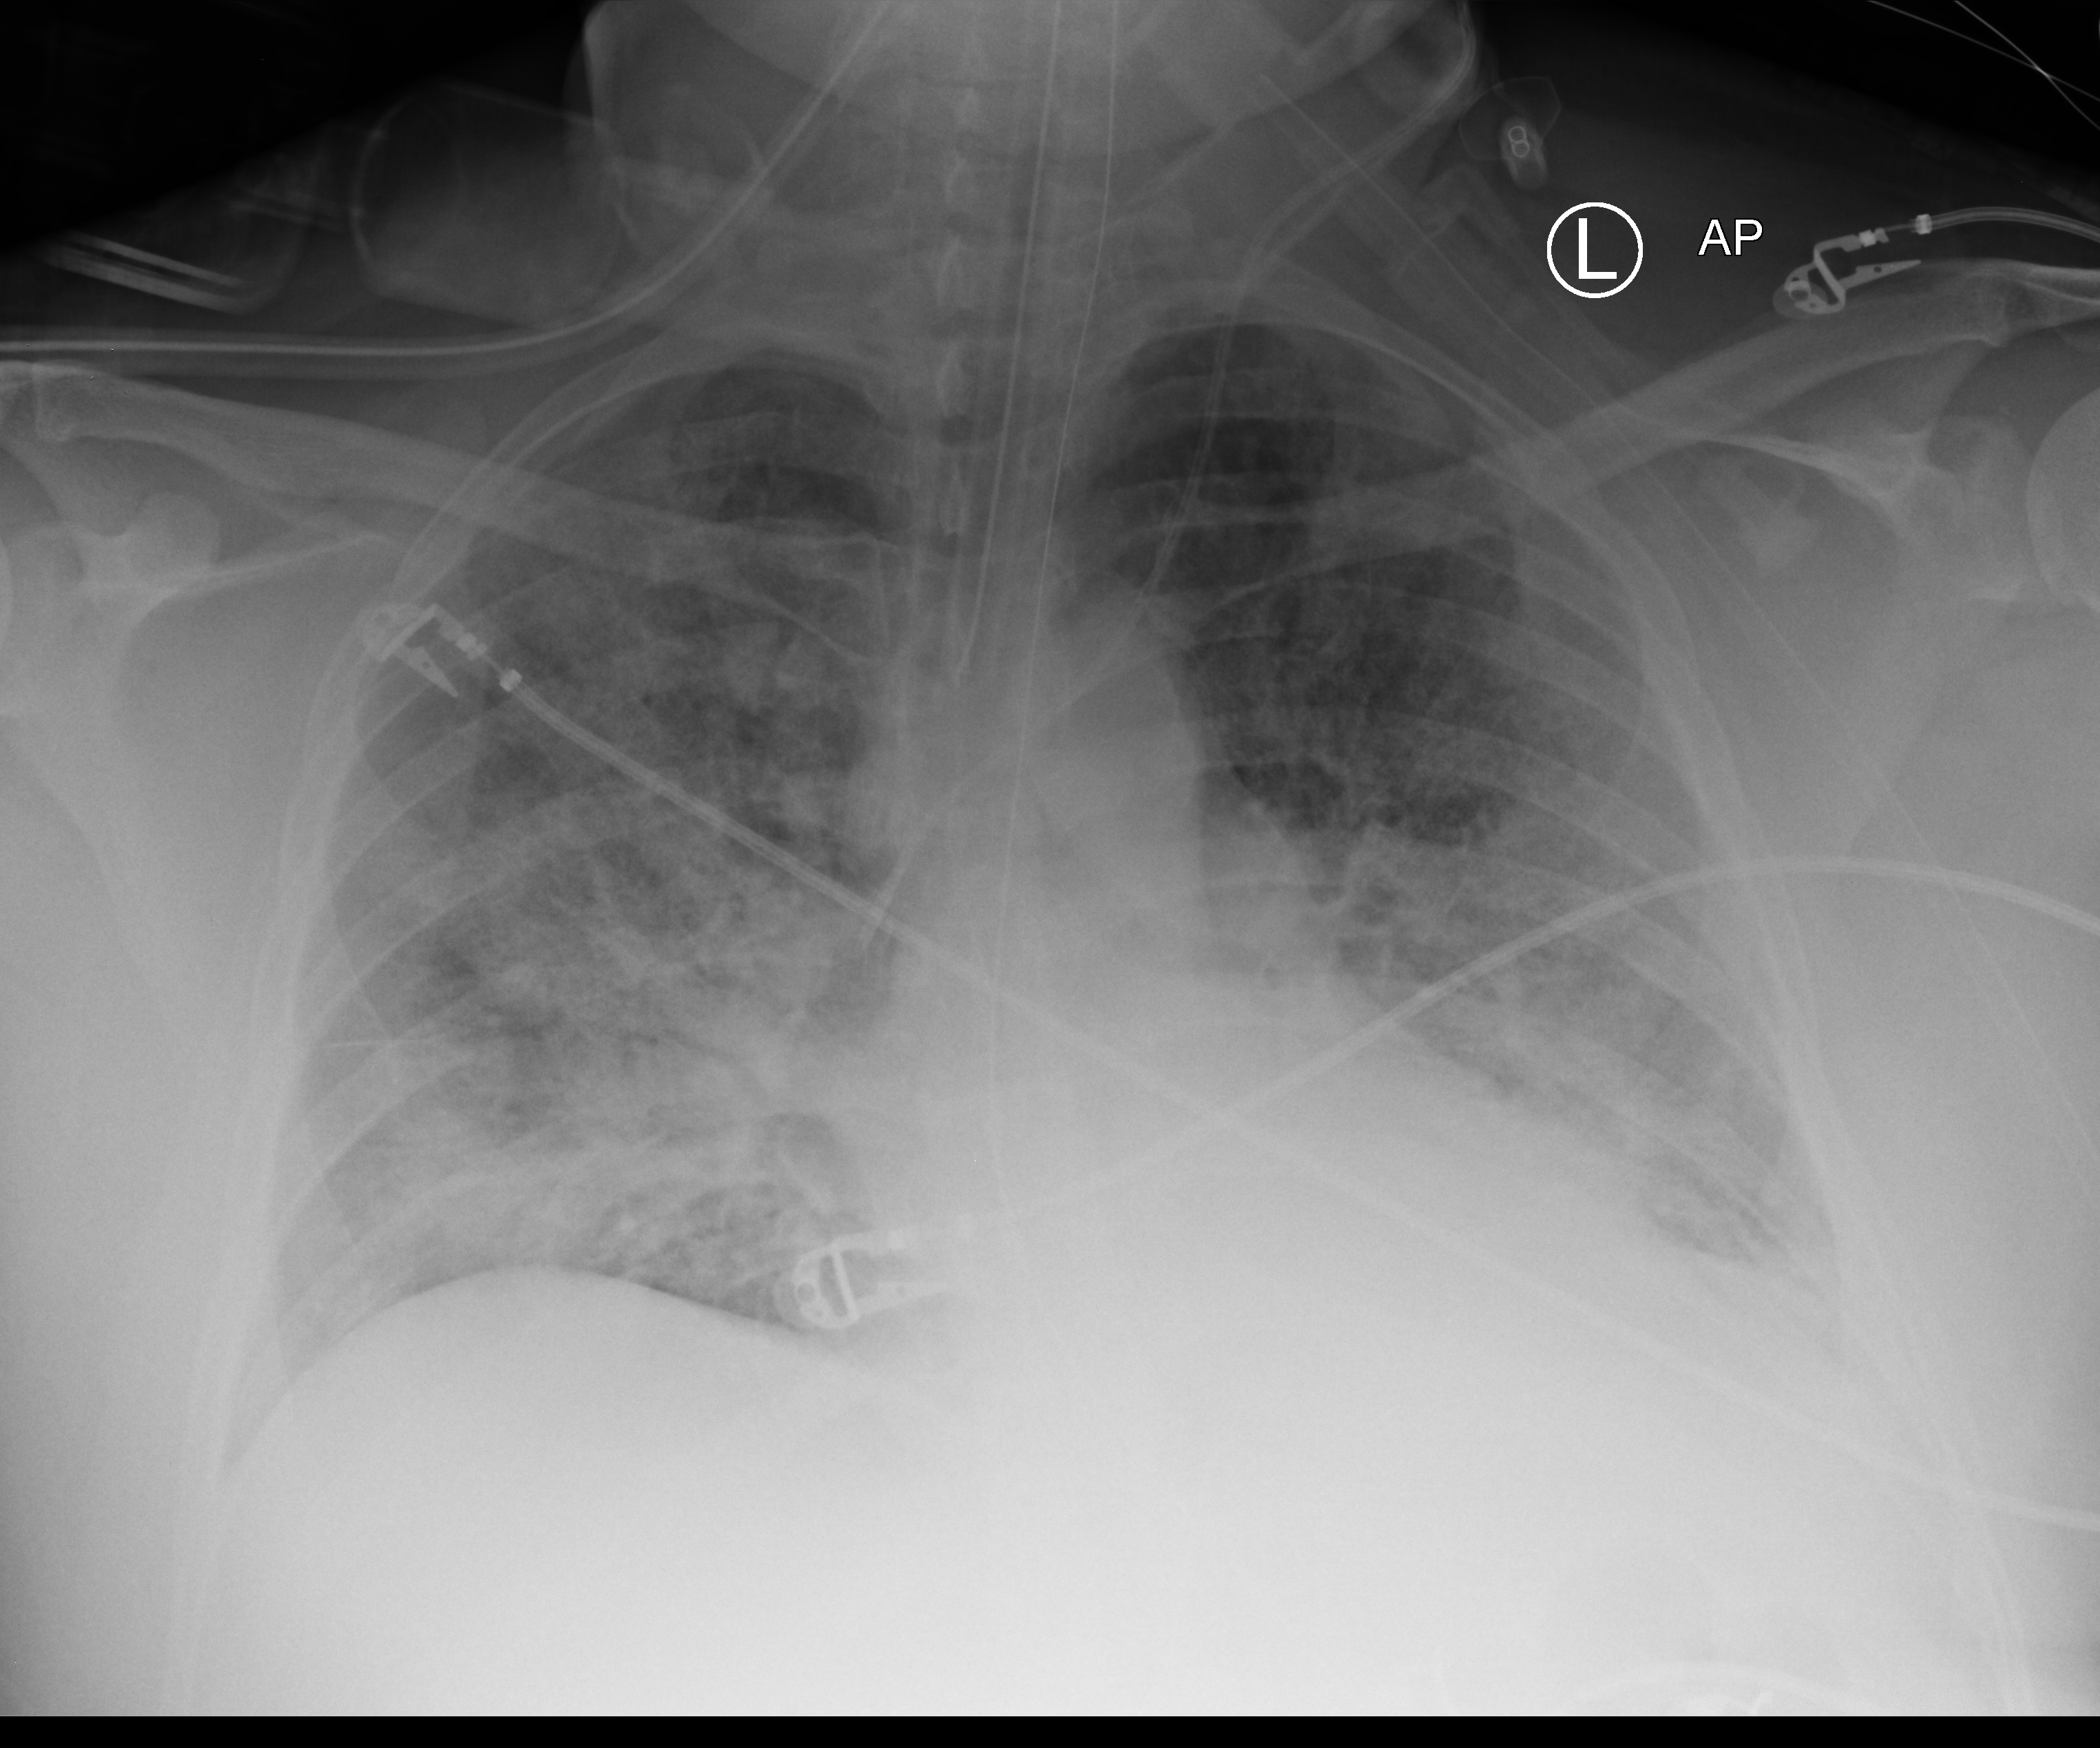
Portable chest radiograph; anteroposterior (AP) projection. Adult patient hospitalised with COVID-19, age 18–59 years.
From the hospital-stay record, not from the radiograph (when in the stay this image was taken is not recorded): length of hospital stay: 16 days.